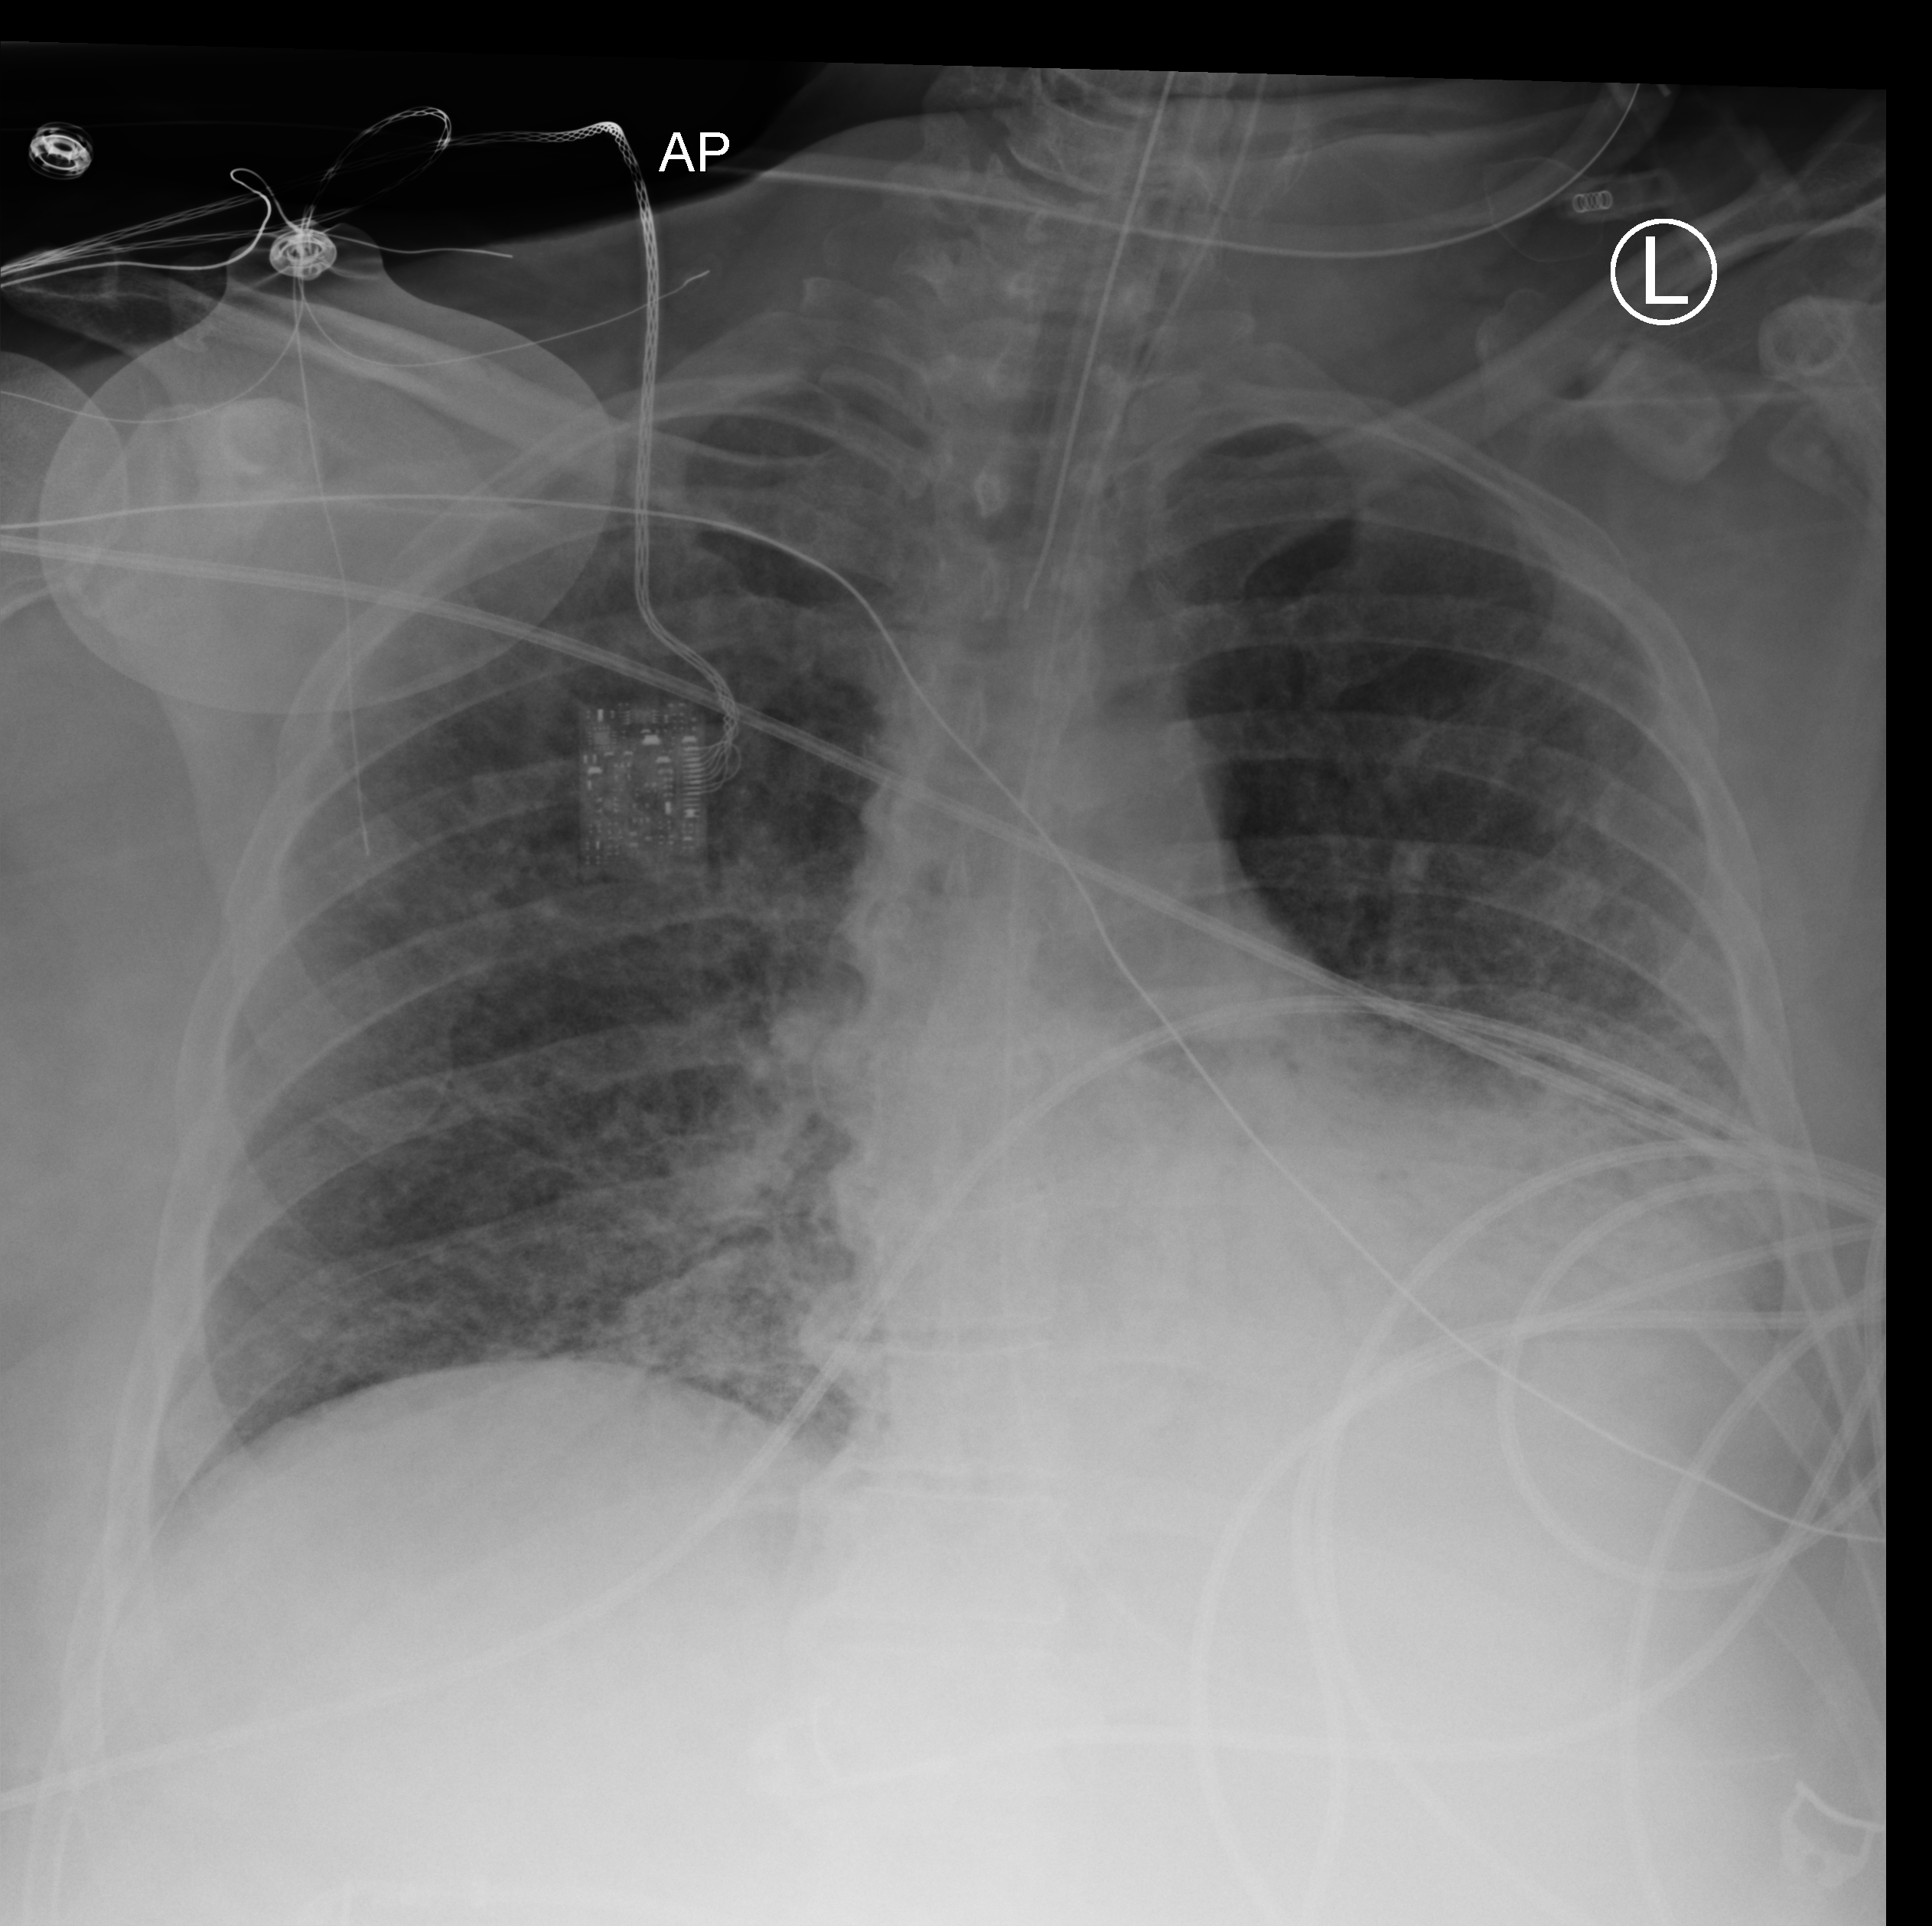
Bedside chest radiograph (computed radiography); anteroposterior (AP) projection. Patient hospitalised with COVID-19, aged 18–59 years.
From the hospital-stay record, not from the radiograph (when in the stay this image was taken is not recorded): mechanically ventilated during this hospital stay: yes; admitted to intensive care during this hospital stay: yes.